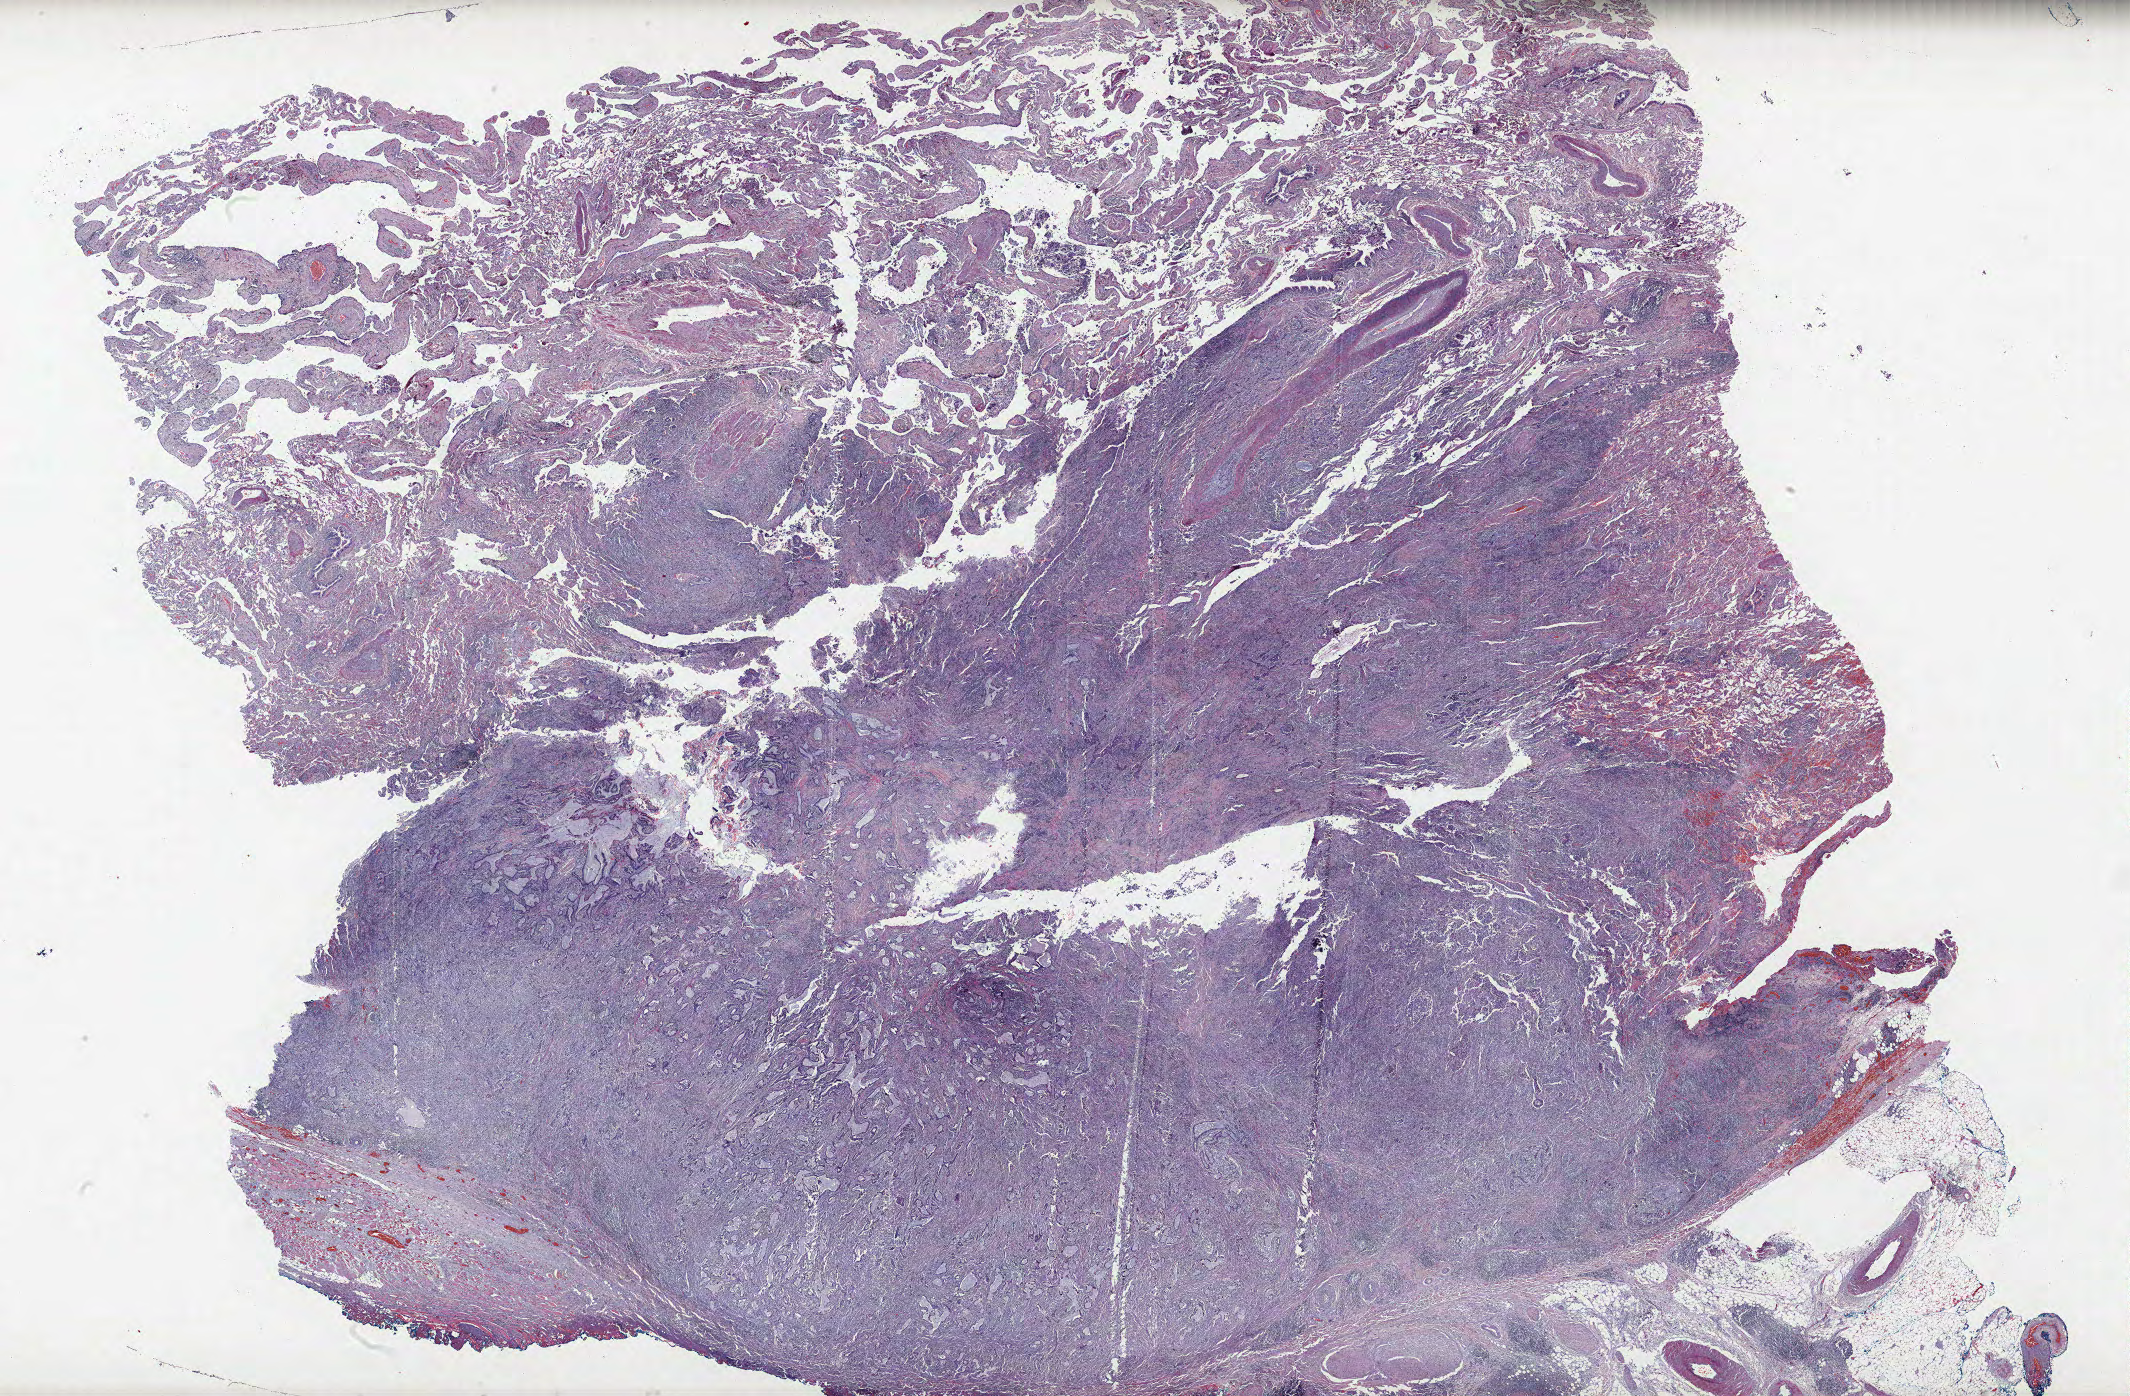
Whole-slide histology image, H&E-stained, shown as a low-resolution overview of the whole scanned area (about 34.1 x 22.3 mm); formalin-fixed paraffin-embedded (FFPE) section; lung. Female patient, aged 56 at enrolment. Grade: well differentiated (G1).
• primary tumour location (clinical record): left upper lobe
• tumour size (pathology): 30 mm
• stage (AJCC 6th edition): IIB
• participant's lung-cancer diagnosis: Mucin-producing adenocarcinoma